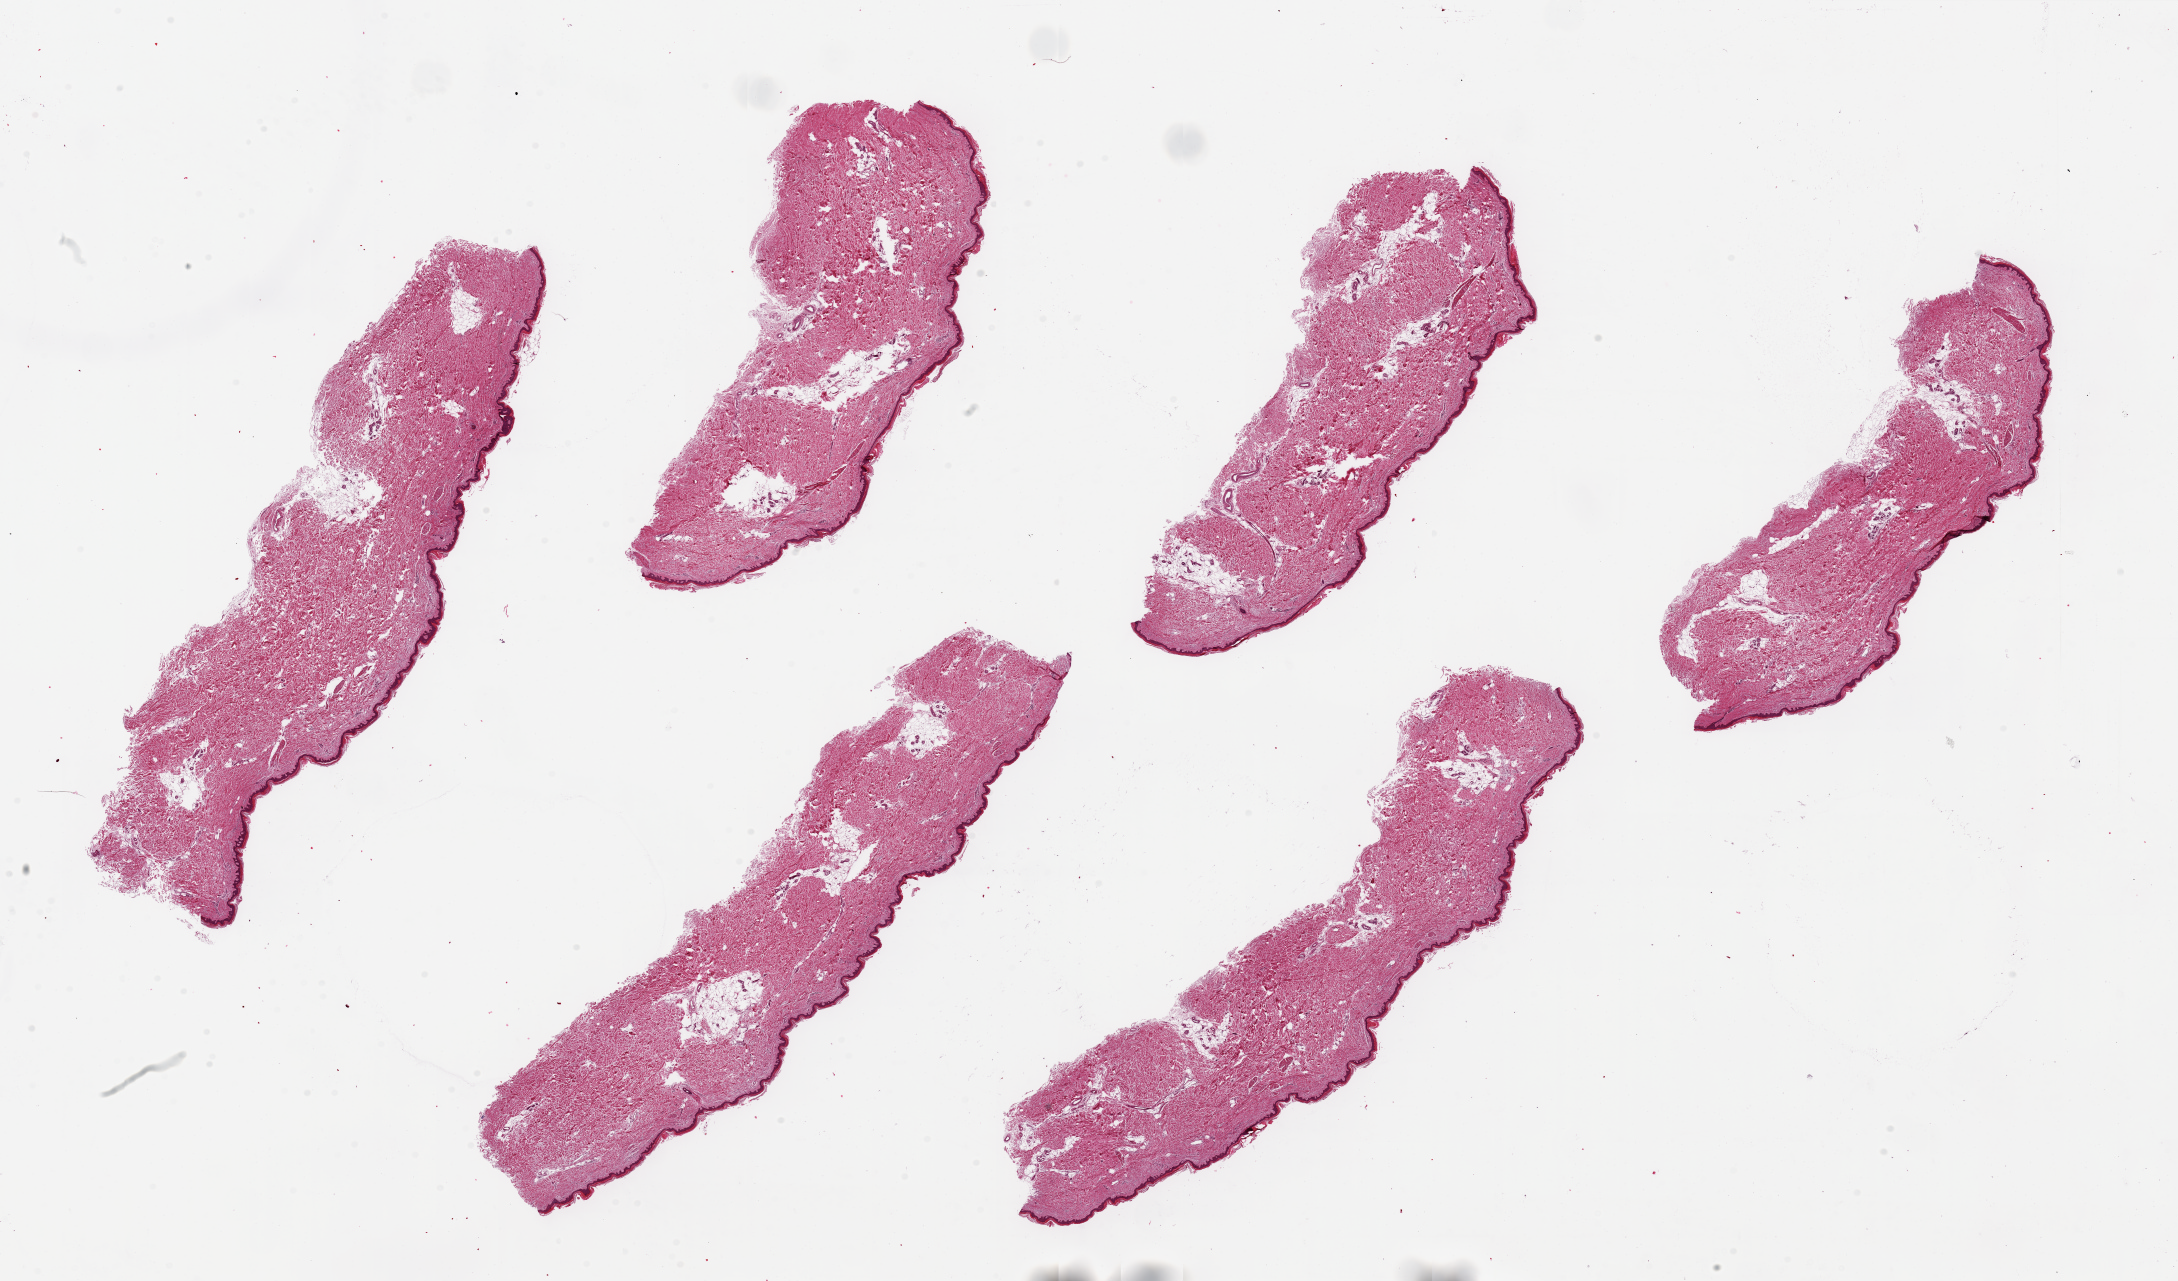
Whole-slide image, H&E stain, whole scanned area (about 34.5 x 20.3 mm) shown as a low-resolution overview. PAXgene-fixed paraffin-embedded (PFPE) section. Sampled site (target tissue): skin of lower leg. Tissue donor sample. Female donor.
Review note (as recorded): 6 pieces, up to 12x4mm; squamous epithelium ~1-2% thickness.